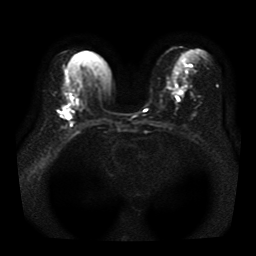
Breast MRI, one axial slice; diffusion-weighted series; image 2 of 4 stored at this slice position (different b-values; order by instance number); 1.5 T; 256 × 256 image matrix, field of view 330 × 330 mm. Female patient.
Outlined on this slice (manually delineated by an expert):
- tumour on diffusion-weighted imaging: bounding box <61,107,72,119> (left, top, right, bottom; pixels)